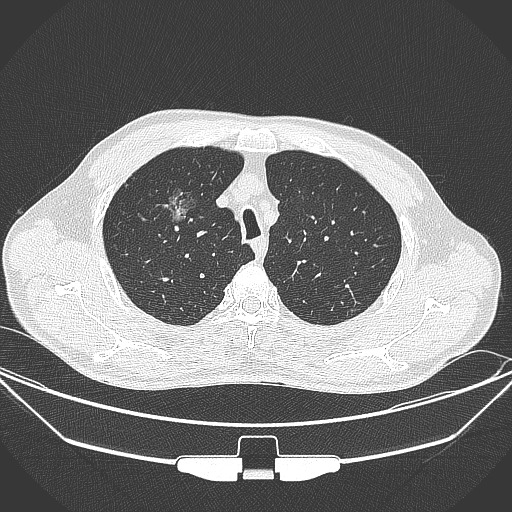
Chest CT, one axial slice; position 276 of 355 along the scan axis; 120 kVp; lung window (W 1500 / L -600 HU); 512 × 512 image matrix, field of view 399 × 399 mm. Male patient, age 67 years. Case-level facts recorded for this patient, not image findings: clinical TNM (as recorded): T1c N0 M0.
Outlined on this slice (rectangle marked by the reading radiologist):
- lung tumour (recorded histology: adenocarcinoma): bounding box [x1, y1, x2, y2] px = [157, 180, 204, 236]